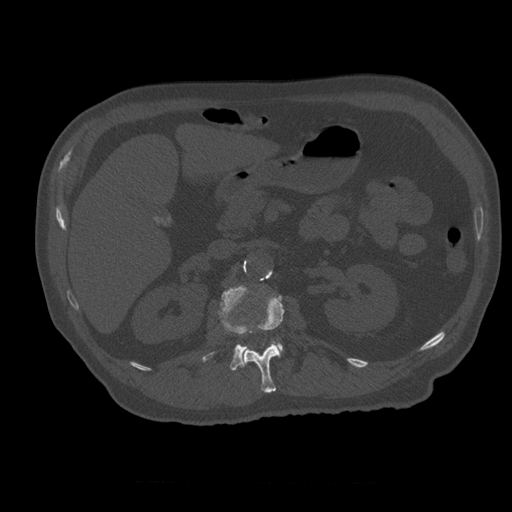
CT including the spine, one axial slice. Slice 229 of 399 in the series (ordered by position). Reconstruction kernel STANDARD. Bone window (W 1800 / L 400 HU). 1.25 mm slice thickness. 512 × 512 image matrix, field of view 407 × 407 mm. Patient age 73 years. Case-level facts recorded for this patient, not image findings: primary cancer: prostate; vertebrae with lytic lesions (as recorded): L2.
Outlined on this slice (semi-automatic segmentation, software-assisted and operator-edited):
- L1 vertebra: bounding box <242,295,285,393> (left, top, right, bottom; pixels)
- L2 vertebra: <202,286,283,371>